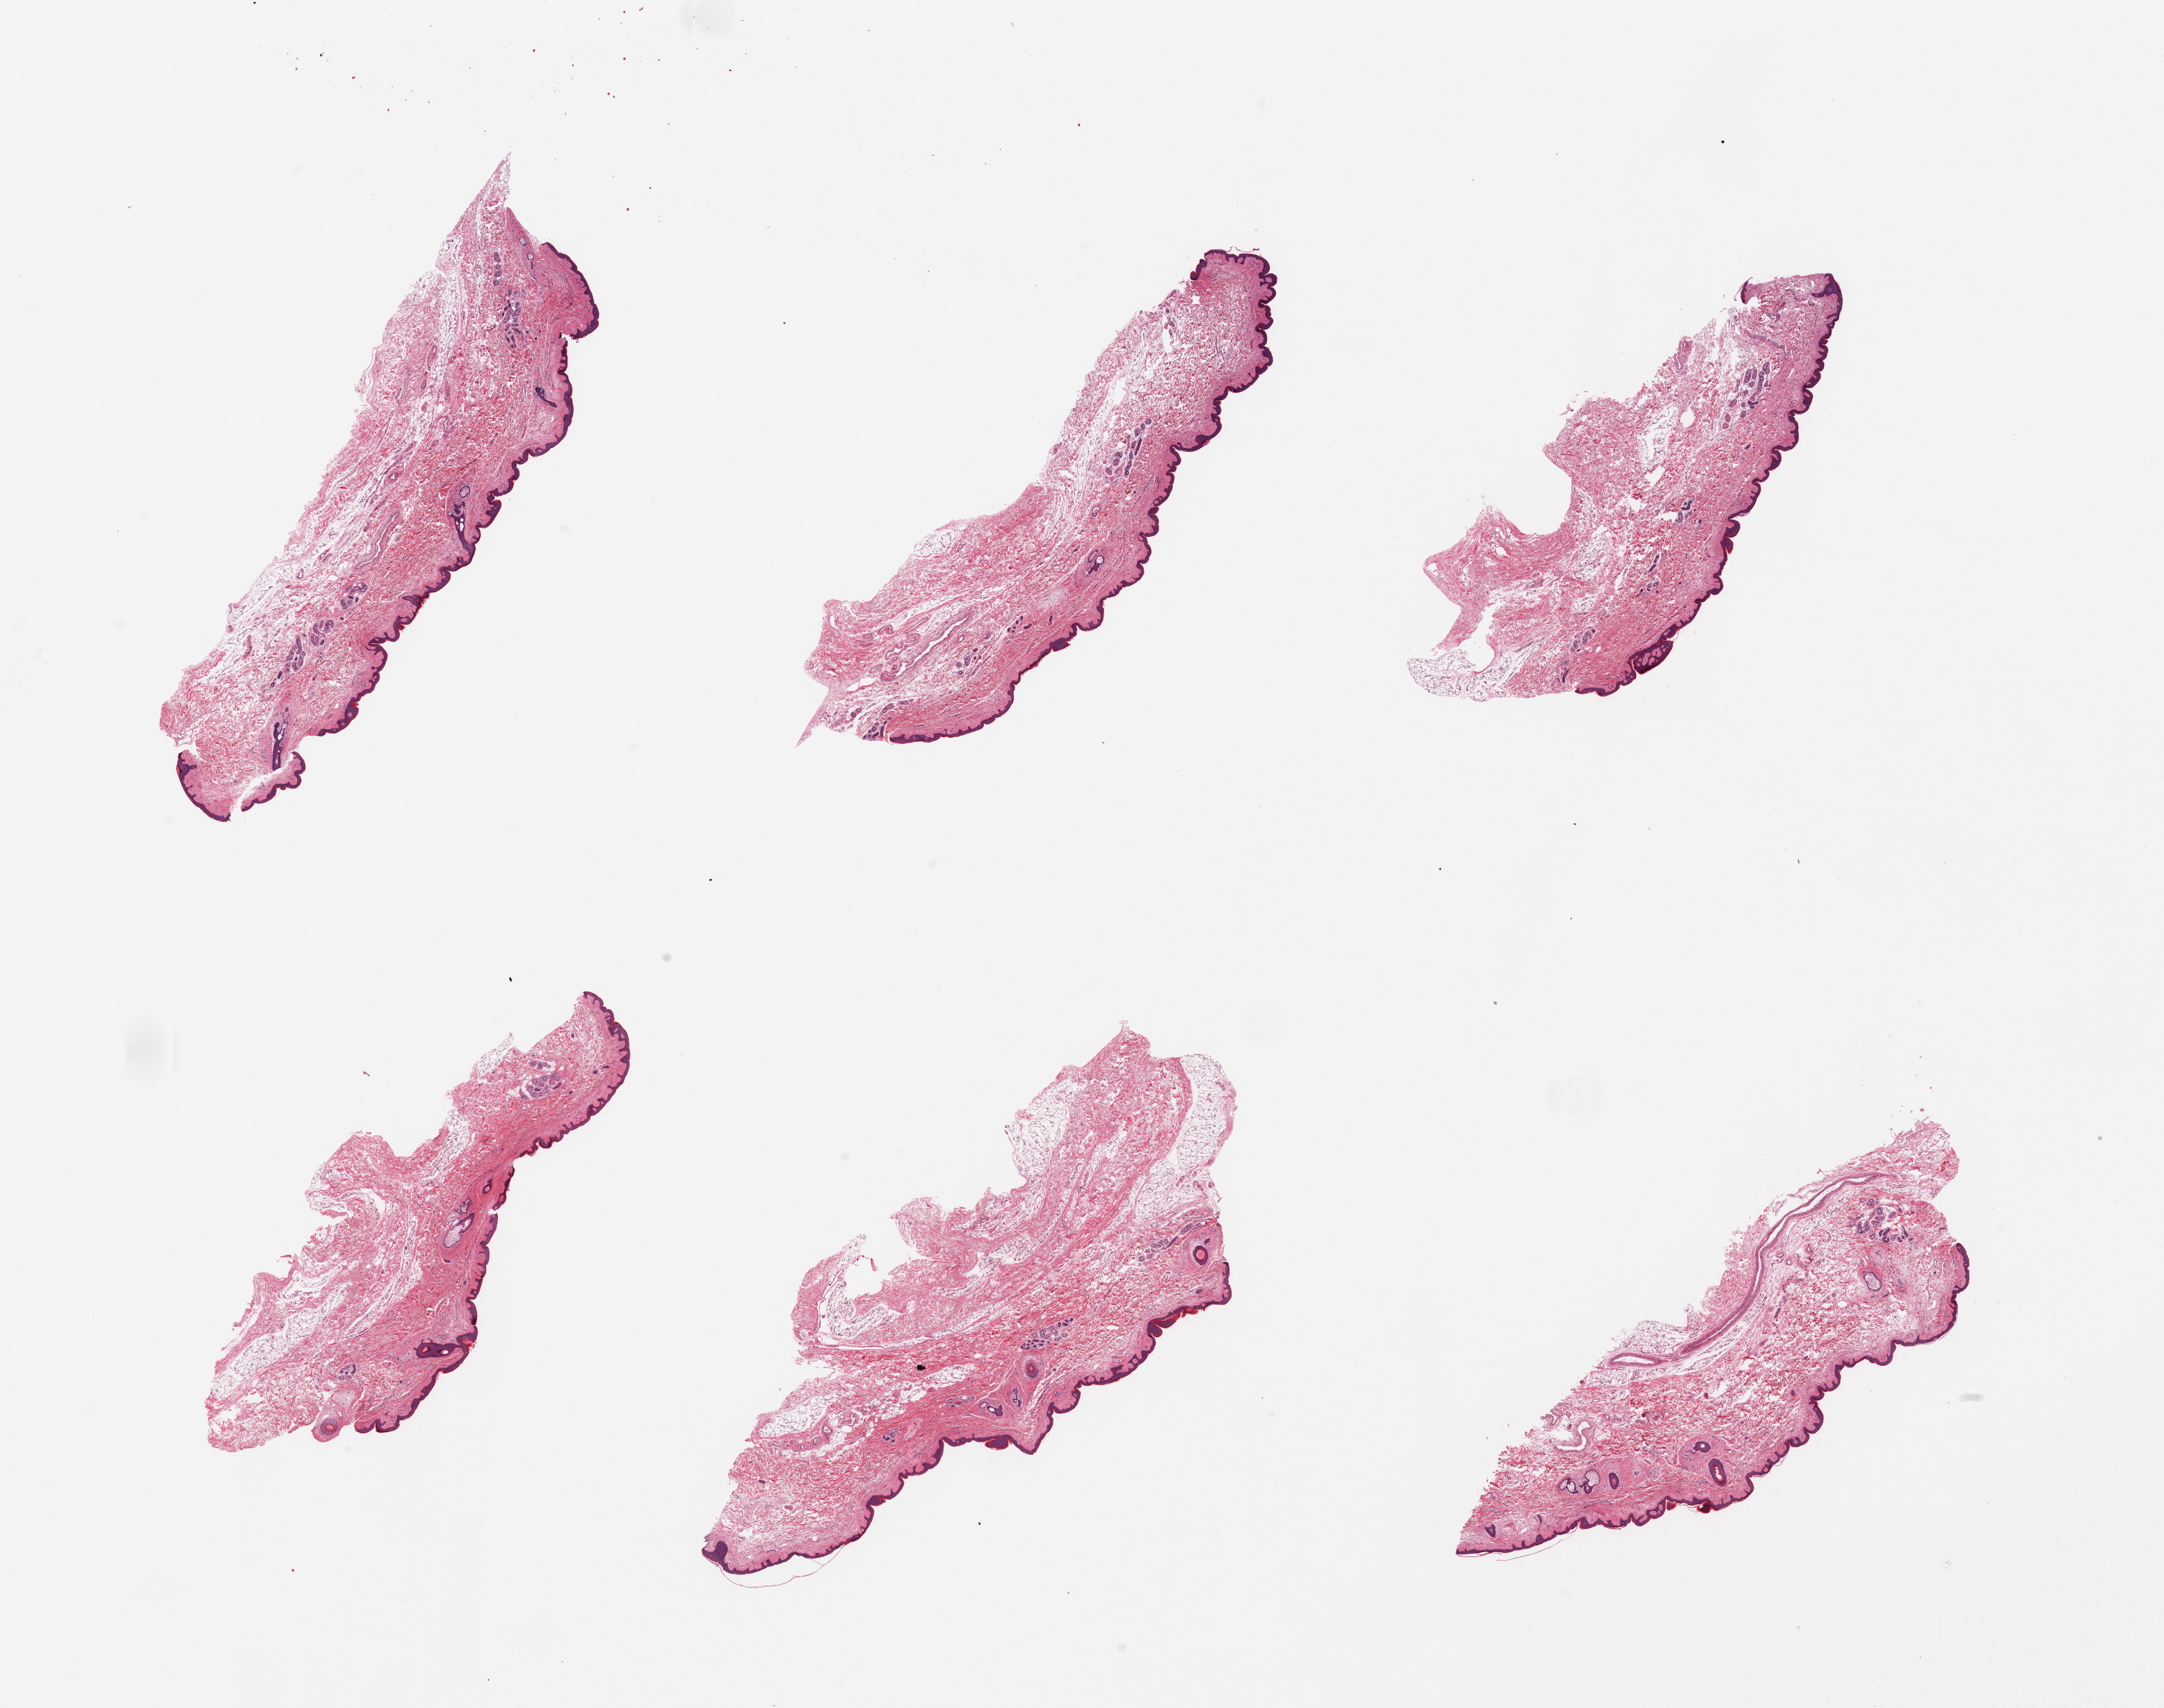
Whole-slide image, H&E stain — a low-resolution overview of the entire scanned area, about 24.6 x 19.4 mm; PAXgene-fixed, paraffin-embedded tissue; section of skin of suprapubic region (target tissue); donor tissue sample. Male donor.
Review note (as recorded): 6 pieces; atrophic; edematous dermis.